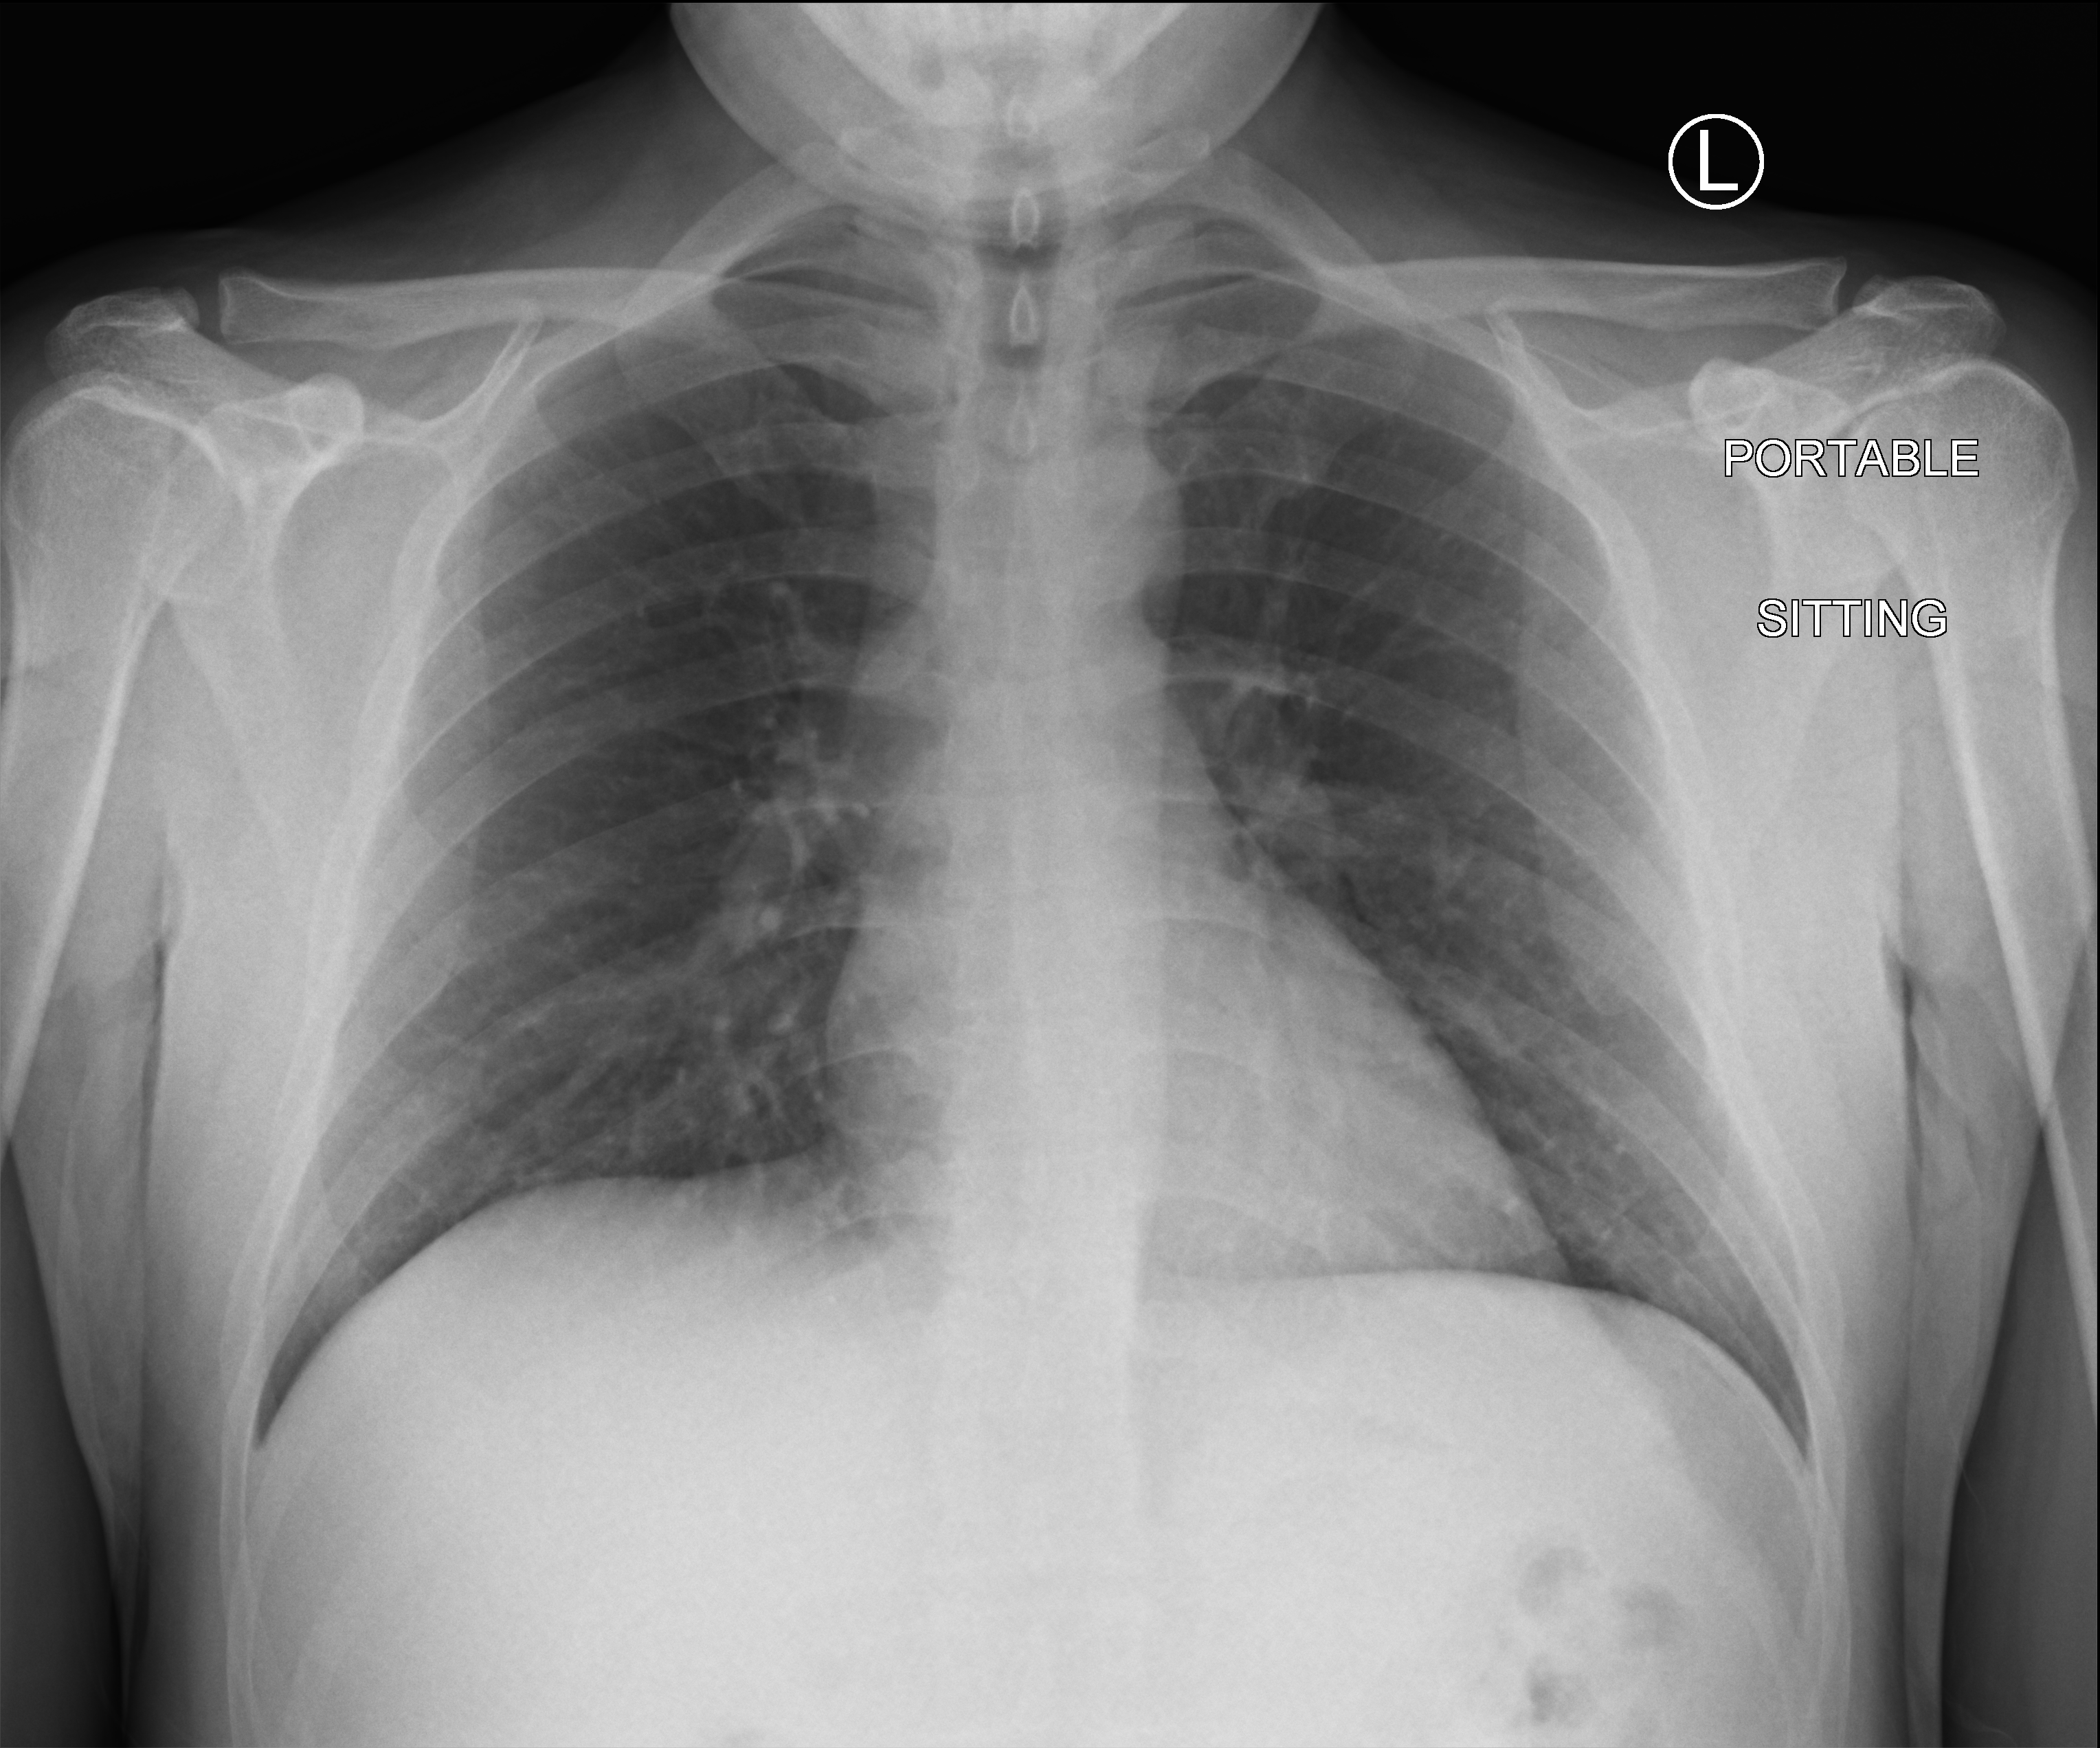
Bedside chest radiograph (computed radiography), anteroposterior (AP) projection. Male patient hospitalised with COVID-19, age 18–59 years.
Admission-level facts for this patient (not findings on this image; timing relative to this image not recorded):
- length of hospital stay: 1 day
- mechanically ventilated during this hospital stay: no
- admitted to intensive care during this hospital stay: no